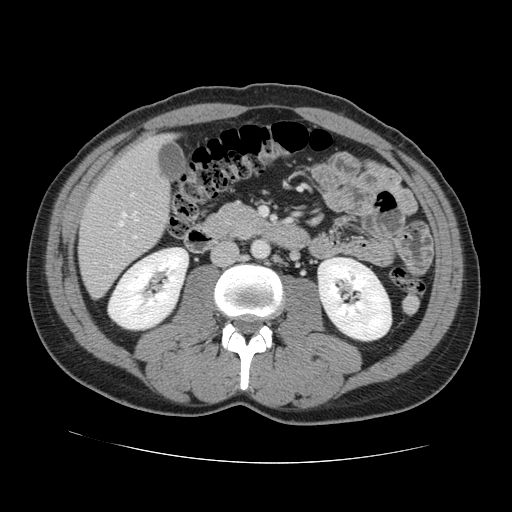
Contrast-enhanced abdominal CT, one axial slice. Position 43 of 131 along the scan axis. 120 kVp. Intravenous contrast given. Soft-tissue window (W 400 / L 40 HU). 2.5 mm slice thickness. 512 × 512 image matrix, field of view 380 × 380 mm. Male patient, age 40 years. Case-level facts recorded for this patient, not image findings: diagnosis: colorectal cancer liver metastases, imaged before liver resection; multiple liver metastases: yes; largest metastasis: 2.9 cm; disease in both lobes: yes.
Annotated regions visible in this slice (outlined manually by an expert reader):
- hepatic veins: bounding box [x1, y1, x2, y2] px = [119, 212, 137, 226]
- liver: [80, 138, 171, 297]
- planned liver remnant (the part of the liver to remain after resection): [130, 138, 163, 164]
- portal vein (with intrahepatic branches): [131, 193, 137, 239]